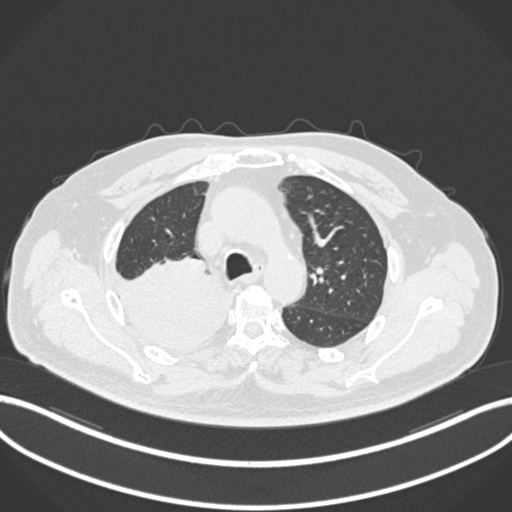
Chest CT, one axial slice. Slice 147 of 218 in the series (ordered by position). Reconstruction kernel B30f. 120 kVp. Lung window (W 1500 / L -600 HU). 1 mm slice thickness. 512 × 512 image matrix, field of view 400 × 400 mm. Patient: male, 68 years. Case-level facts recorded for this patient, not image findings: clinical TNM (as recorded): T2a N0 M0.
Structures marked on this image (rectangle marked by the reading radiologist):
- lung tumour (recorded histology: adenocarcinoma): bounding box <114,253,231,353> (left, top, right, bottom; pixels)